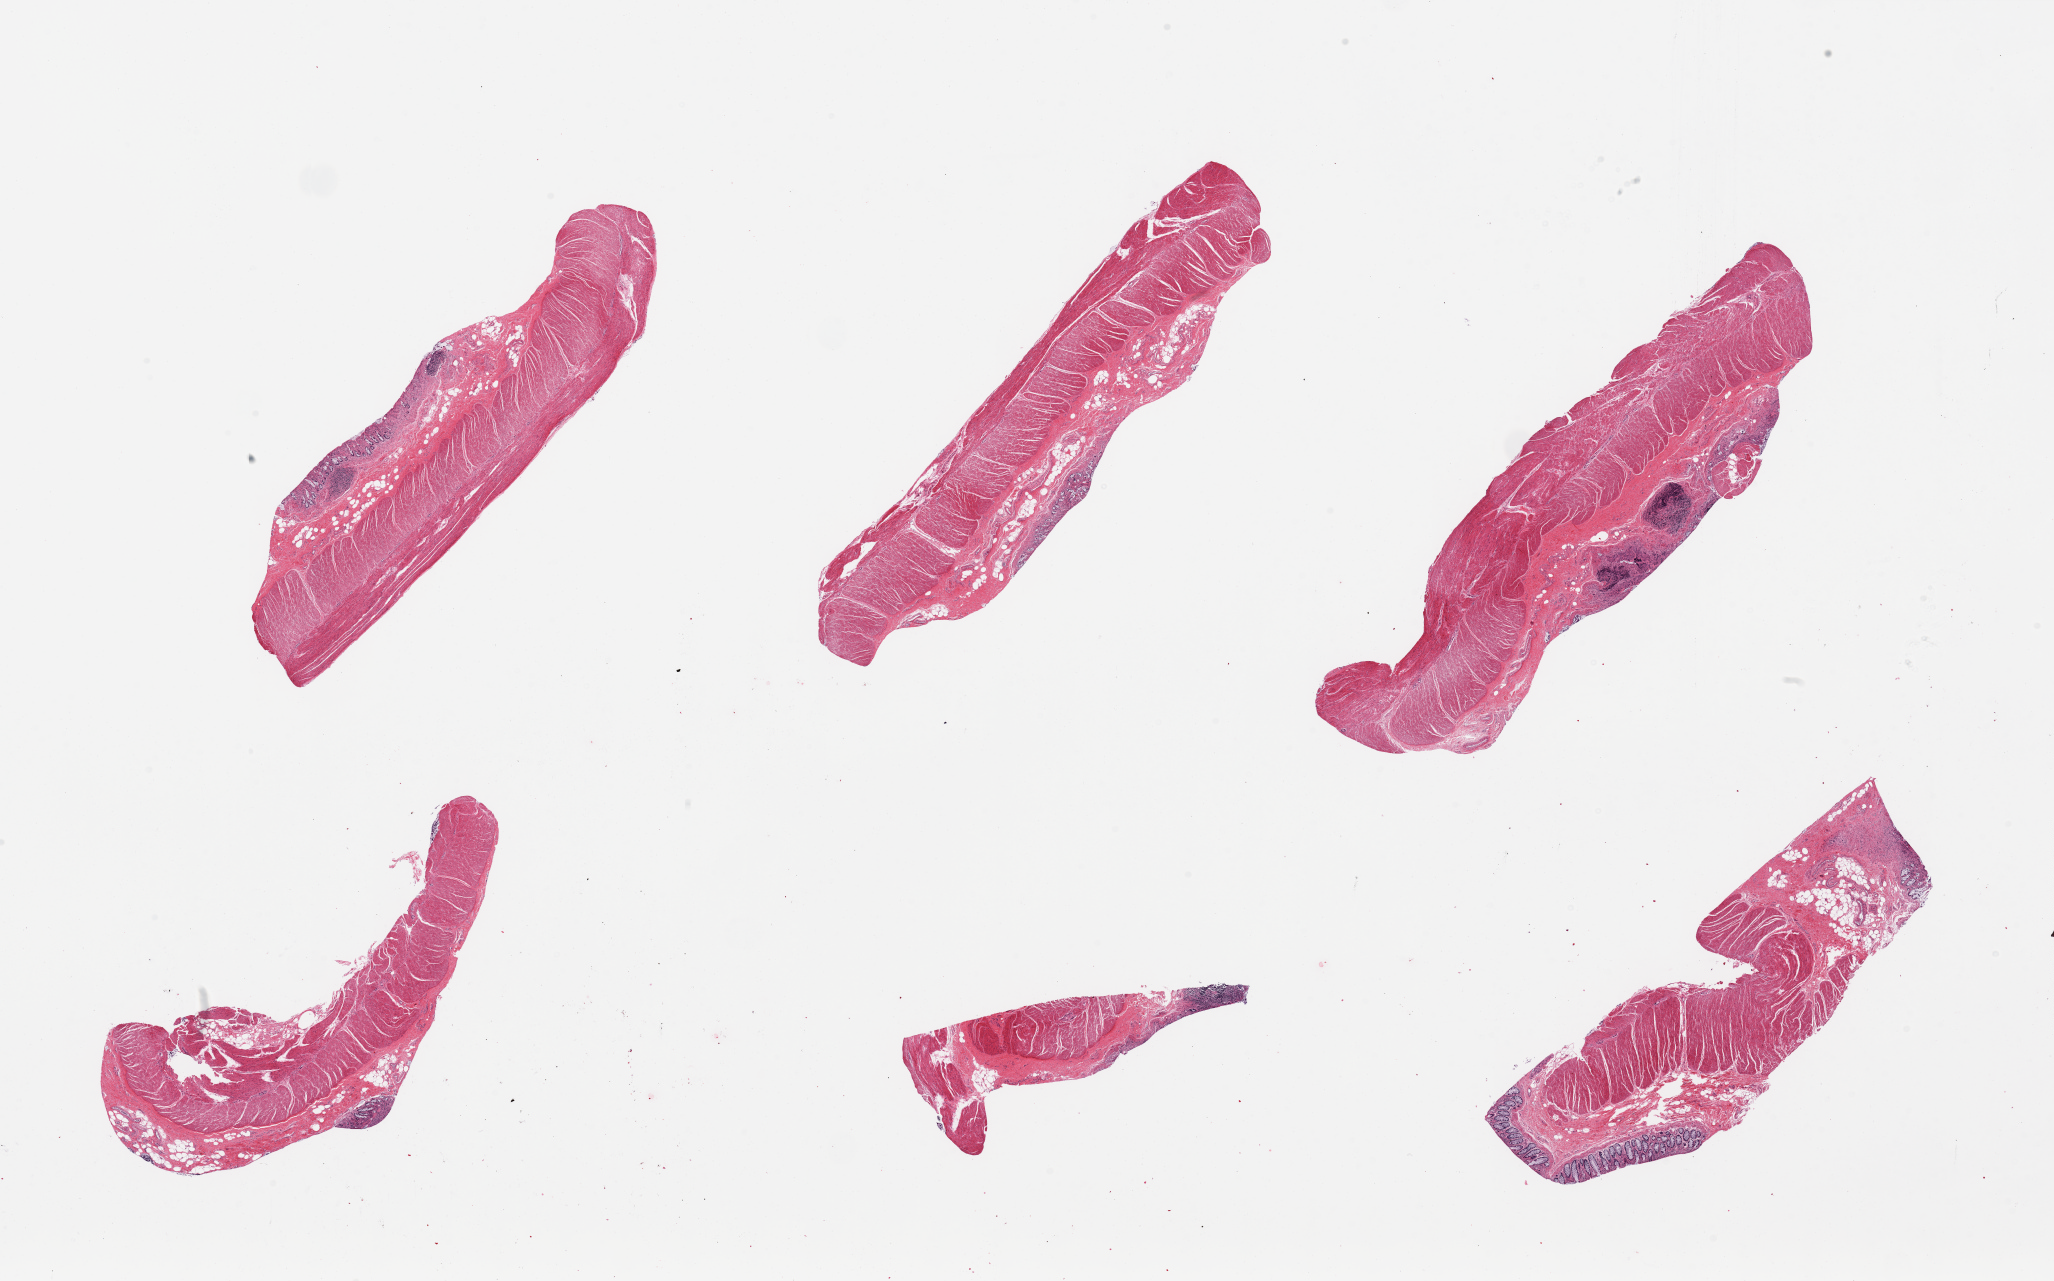
Whole-slide image, haematoxylin and eosin stain — shown as a low-resolution overview of the whole scanned area (about 32.5 x 20.3 mm). PAXgene-fixed paraffin-embedded (PFPE) section. Target tissue: sigmoid colon. Donor tissue sample. Donor: male.
* reviewer comment on this tissue sample: 6 pieces, trace 'contaminant' mucosa, ~5% total